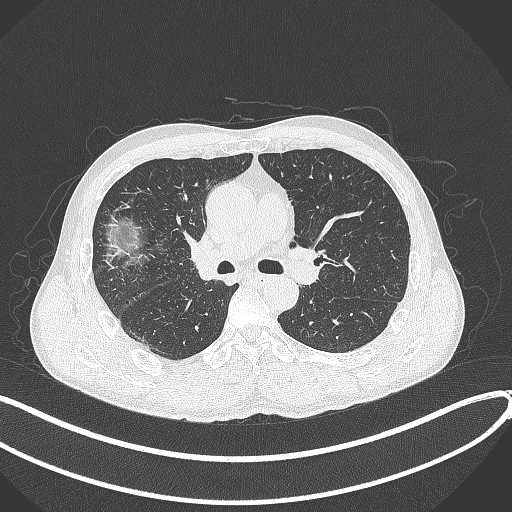
Chest CT, one axial slice. Position 232 of 409 along the scan axis. Reconstruction kernel B70f. Lung window (W 1500 / L -600 HU). 1 mm slice thickness. 512 × 512 image matrix, field of view 400 × 400 mm. Male patient, age 53 years. From the clinical record (not read from this slice): clinical TNM (as recorded): T1b N0 M0.
Outlined on this slice (rectangle marked by the reading radiologist):
- lung tumour (recorded histology: squamous cell carcinoma): bounding box (x1, y1, x2, y2) in pixels: (181, 227, 223, 280)